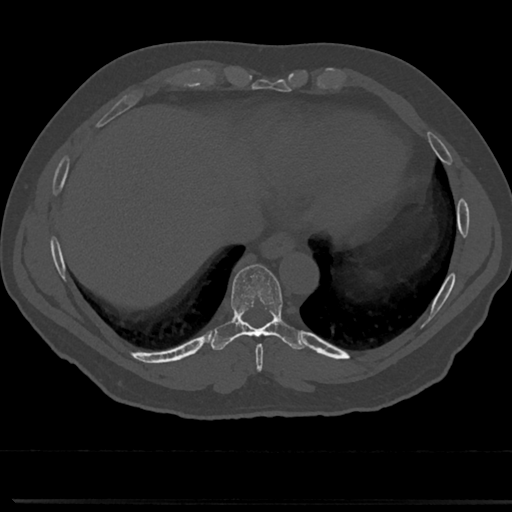
CT including the spine, one axial slice. Slice 311 of 817 in the series (ordered by position). Reconstruction kernel Br40s/3. Bone window (W 1800 / L 400 HU). 0.5 mm slice thickness. 512 × 512 image matrix. Male patient, age 61 years. Case-level facts recorded for this patient, not image findings: primary cancer: prostate.
Outlined on this slice (semi-automatic segmentation, software-assisted and operator-edited):
- T8 vertebra: bounding box [x1, y1, x2, y2] px = [231, 270, 290, 353]
- T9 vertebra: [233, 267, 282, 328]